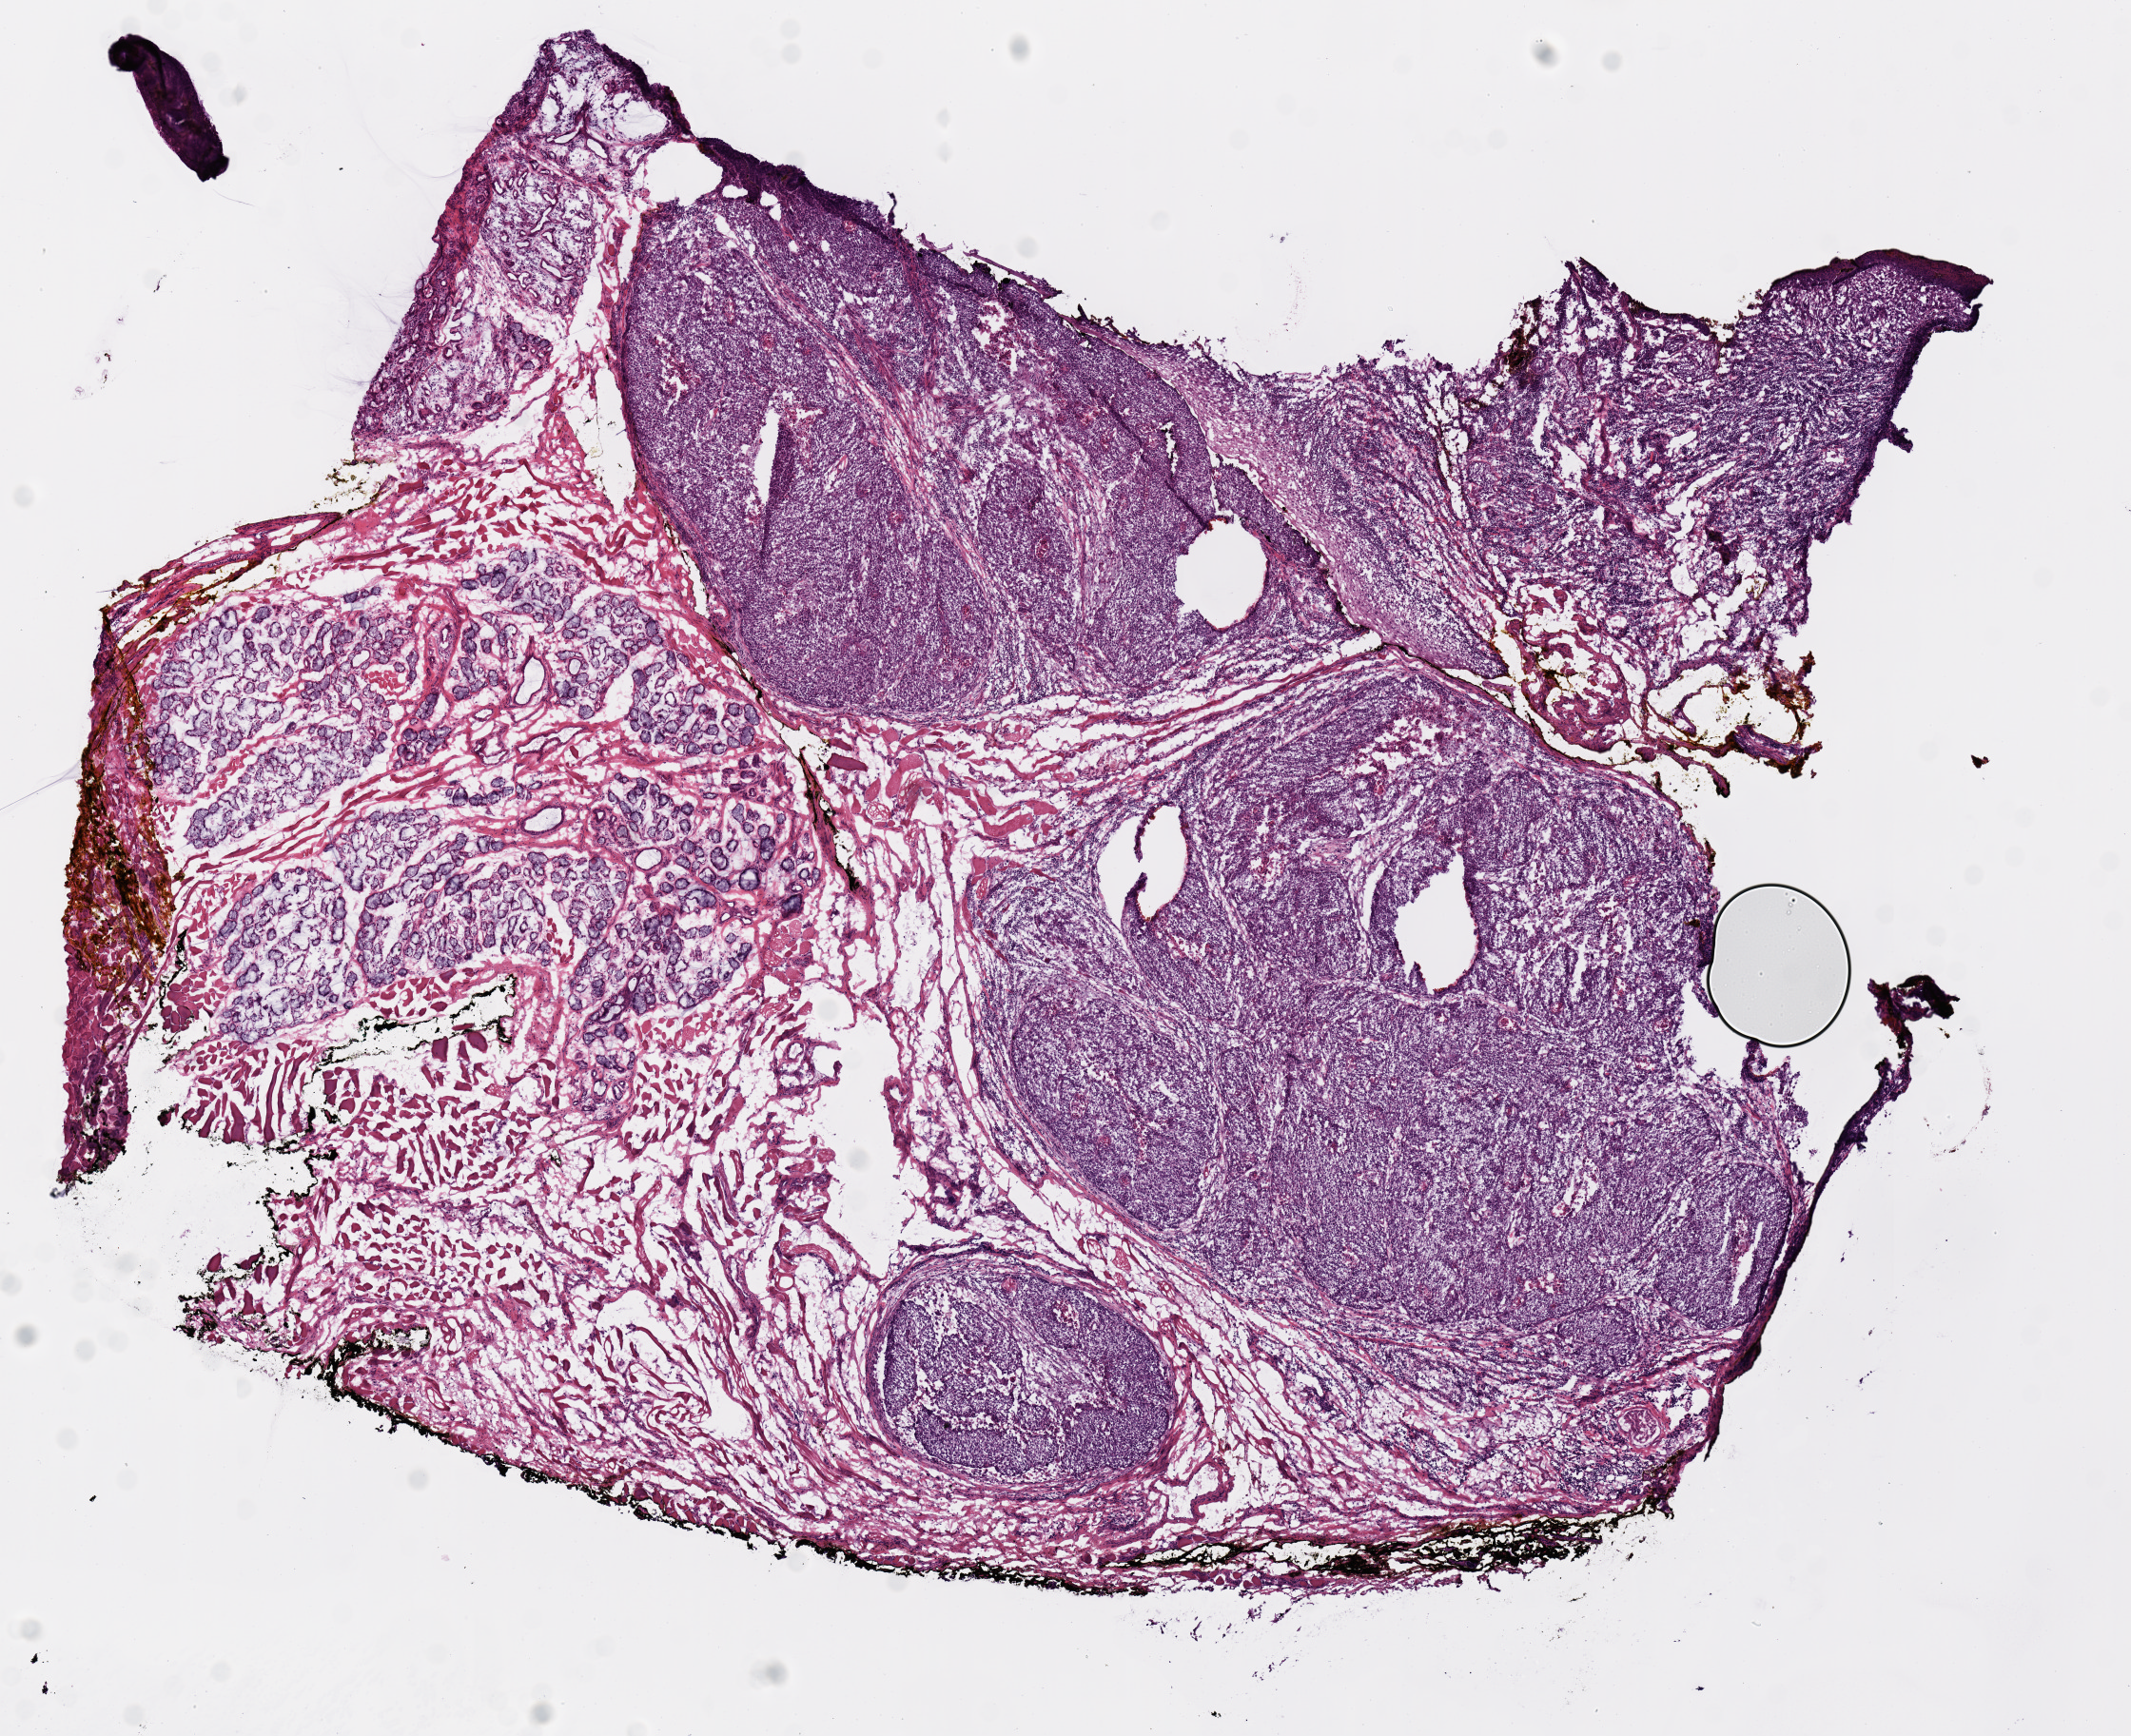
Whole-slide histology image, H&E — shown as a low-resolution overview of the whole scanned area (about 8.9 x 7.2 mm, acquisition: 20x scan); frozen section from the top of the tissue portion; sample: primary tumour, head and neck. Male patient; age at initial diagnosis 58 years. Histologic grade: G4 (undifferentiated). Composition of this section per pathologist review: tumour nuclei 70%, necrosis 0%.
* diagnosis: Basaloid squamous cell carcinoma
* AJCC pathologic stage: III (7th edition)